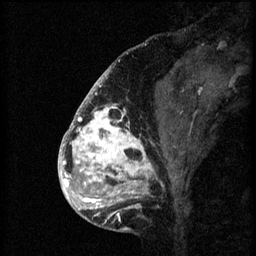
Breast MRI (dynamic contrast-enhanced), one sagittal slice; position 24 of 60 along the scan axis; 3 images stored at this slice position (order not interpretable as contrast timing); 1.5 T; TE 4.2 ms, TR 8.2 ms; 2 mm slice thickness; 256 × 256 image matrix, field of view 180 × 180 mm. Patient: female, 41 years.
Structures marked on this image (semi-automatically segmented with operator editing):
- analysis volume of interest (the breast-tissue region the enhancement analysis was run in; not a lesion): bounding box (x1, y1, x2, y2) in pixels: (72, 108, 176, 205)
- tumour enhancement mask (voxels above the 70 % enhancement threshold inside the analysis volume of interest): (72, 108, 155, 205)